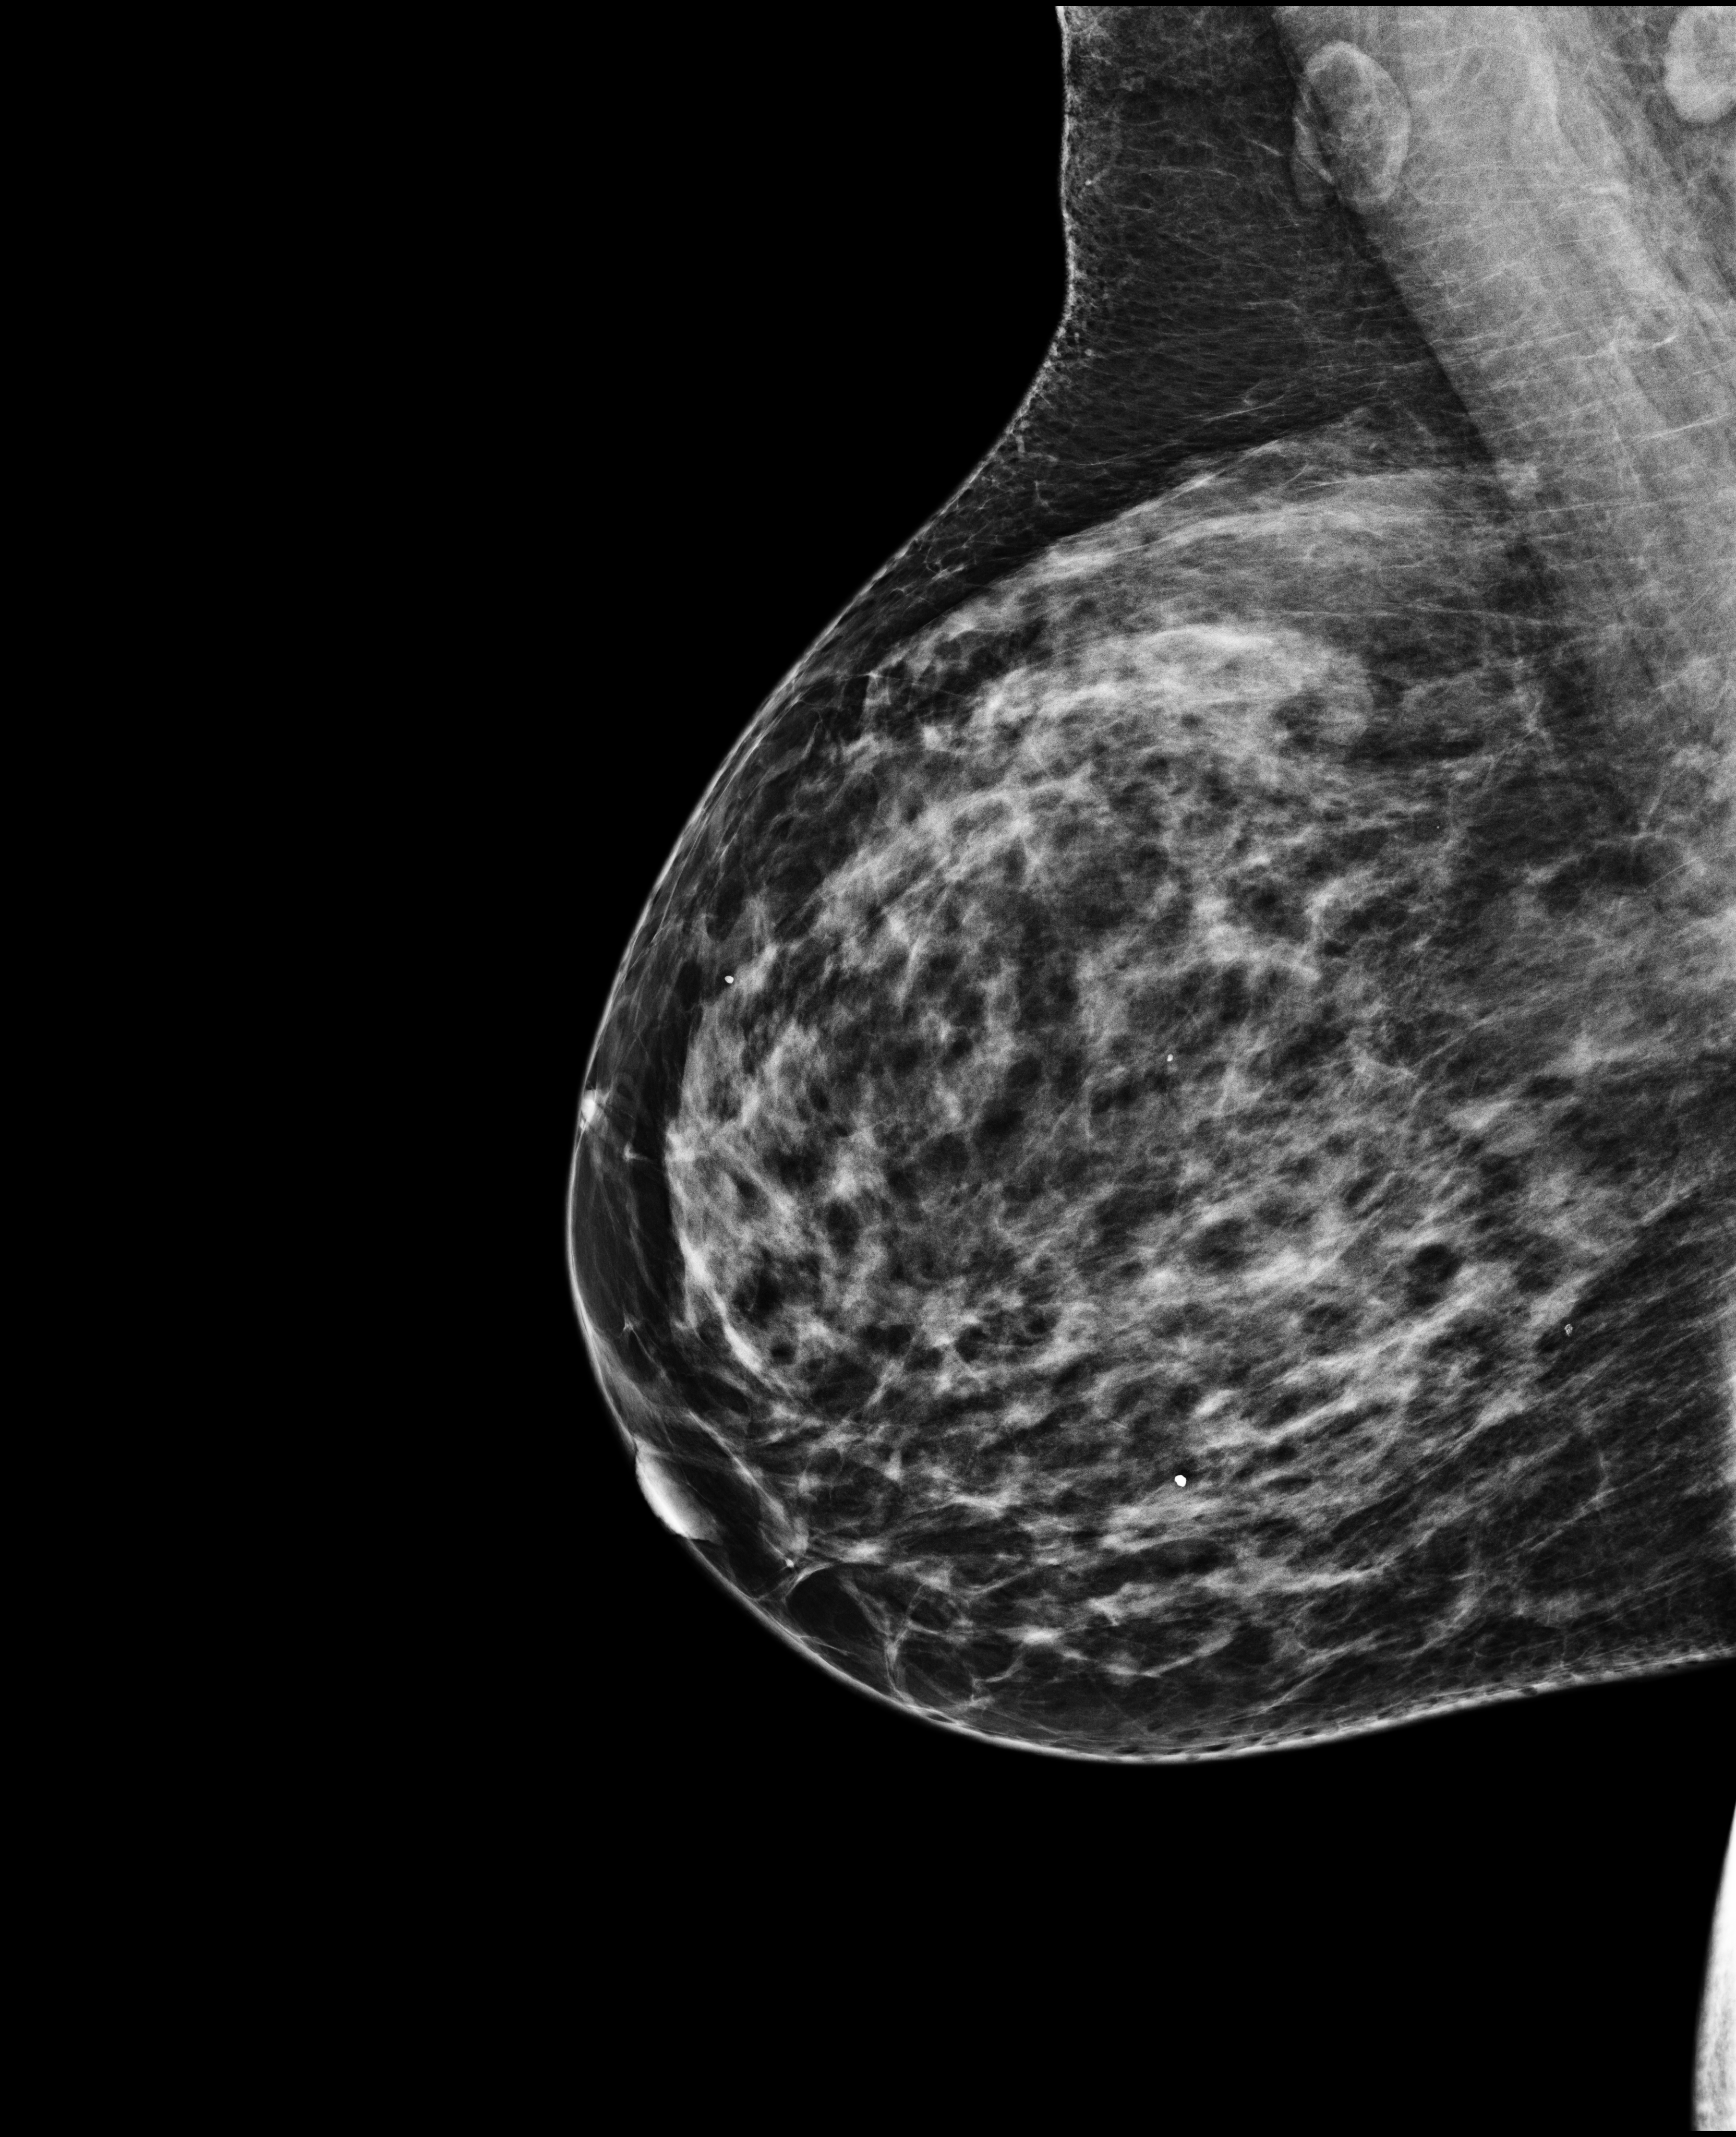
Digital mammogram (FFDM); right breast; medio-lateral oblique projection; annual screening mammography examination; system: Selenia Dimensions. Female patient, age 44 years.
BI-RADS breast density category at the screening exam (both breasts, scale 1–4): 3. Final BI-RADS category for the screening round (tomosynthesis exam, both breasts): category 2. Recall: no recall after this screen.